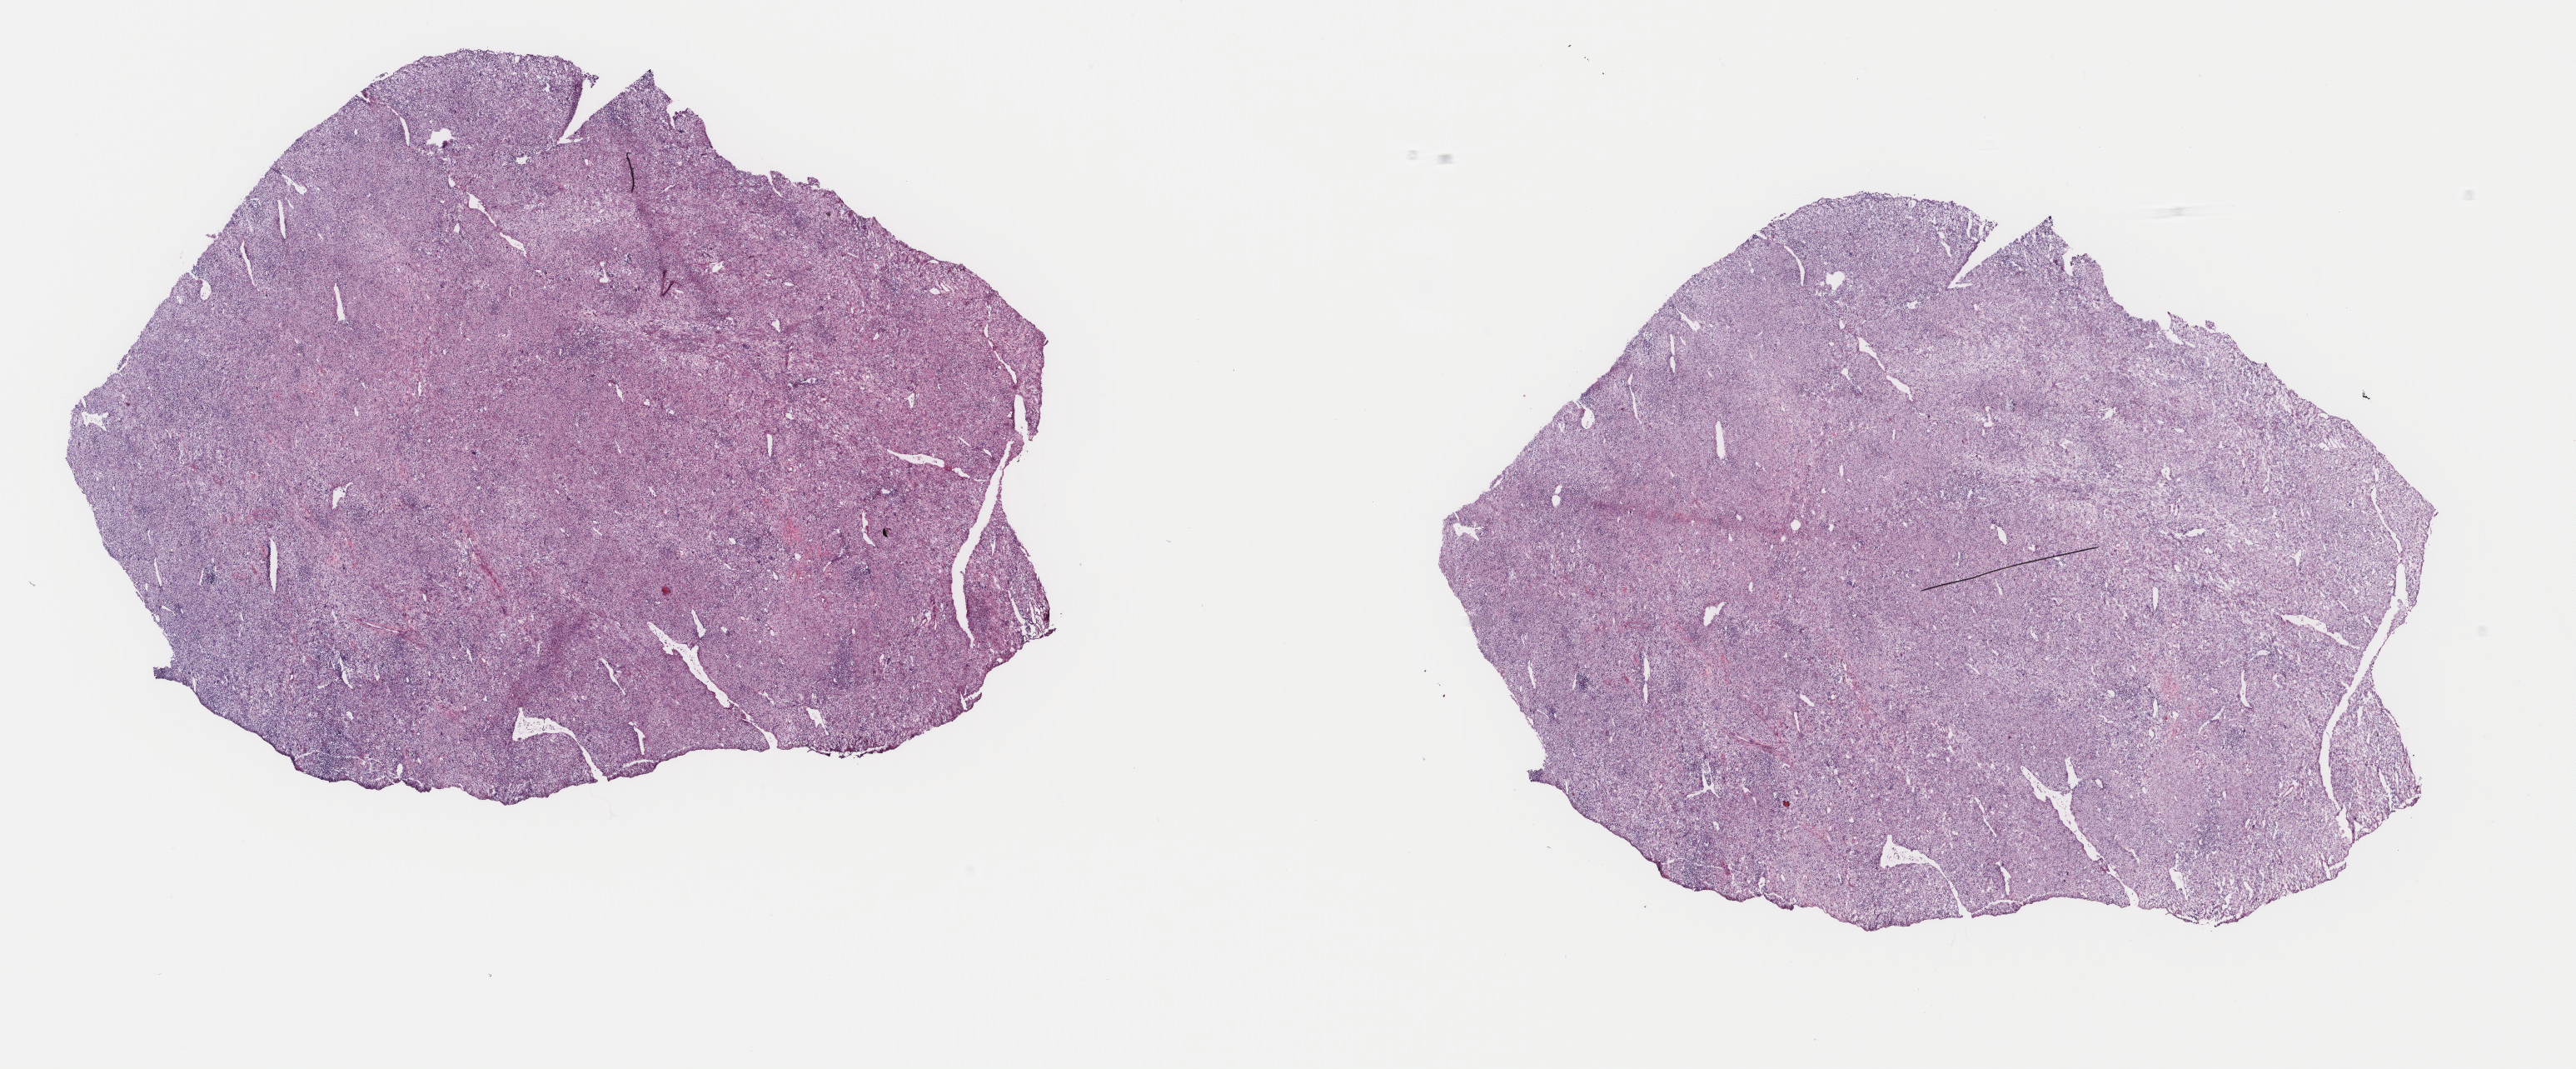
Digitized H&E-stained tissue section (whole slide) — whole scanned area (about 24.6 x 10.2 mm) shown as a low-resolution overview; frozen section; connective, subcutaneous and other soft tissues, primary tumour sample. Patient: female, age at initial diagnosis 50 years. Composition of this section per pathologist review: tumour cells 80%, tumour nuclei 100%, normal cells 0%, stromal cells 20%, necrosis 0%. Inflammatory infiltration, as recorded: lymphocyte infiltration 2%, monocyte infiltration 2%, neutrophil infiltration 0%.
• histologic diagnosis: Pleomorphic liposarcoma